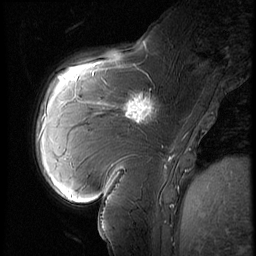
Breast MRI (dynamic contrast-enhanced), one sagittal slice; position 21 of 60 along the scan axis; 3 images stored at this slice position (order not interpretable as contrast timing); 1.5 T; TE 4.2 ms, TR 9 ms; 2.5 mm slice thickness; 256 × 256 image matrix, field of view 180 × 180 mm. Female patient, age 57 years. From the clinical record (not read from this slice): setting: breast cancer imaged before/during neoadjuvant chemotherapy; receptor status: triple-negative.
Outlined on this slice (semi-automatically segmented with operator editing):
- analysis volume of interest (the breast-tissue region the enhancement analysis was run in; not a lesion): box from (x=114, y=83) to (x=170, y=131) px
- tumour enhancement mask (voxels above the 140 % enhancement threshold inside the analysis volume of interest): (x=125, y=94)–(x=154, y=123)